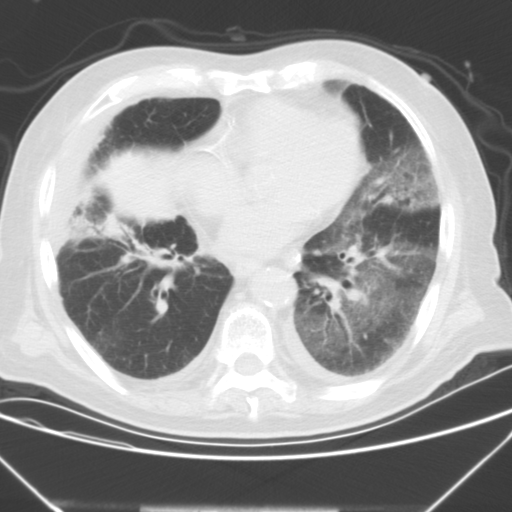
Chest CT, one axial slice. Slice 12 of 43 in the series (ordered by position). 120 kVp. Lung window (W 1500 / L -600 HU). 512 × 512 image matrix, field of view 343 × 343 mm. Male patient, age 85 years. Case-level facts recorded for this patient, not image findings: clinical TNM (as recorded): T4 N3 M2.
Outlined on this slice (rectangle marked by the reading radiologist):
- lung tumour (recorded histology: squamous cell carcinoma): bounding box (x1, y1, x2, y2) in pixels: (103, 151, 188, 245)